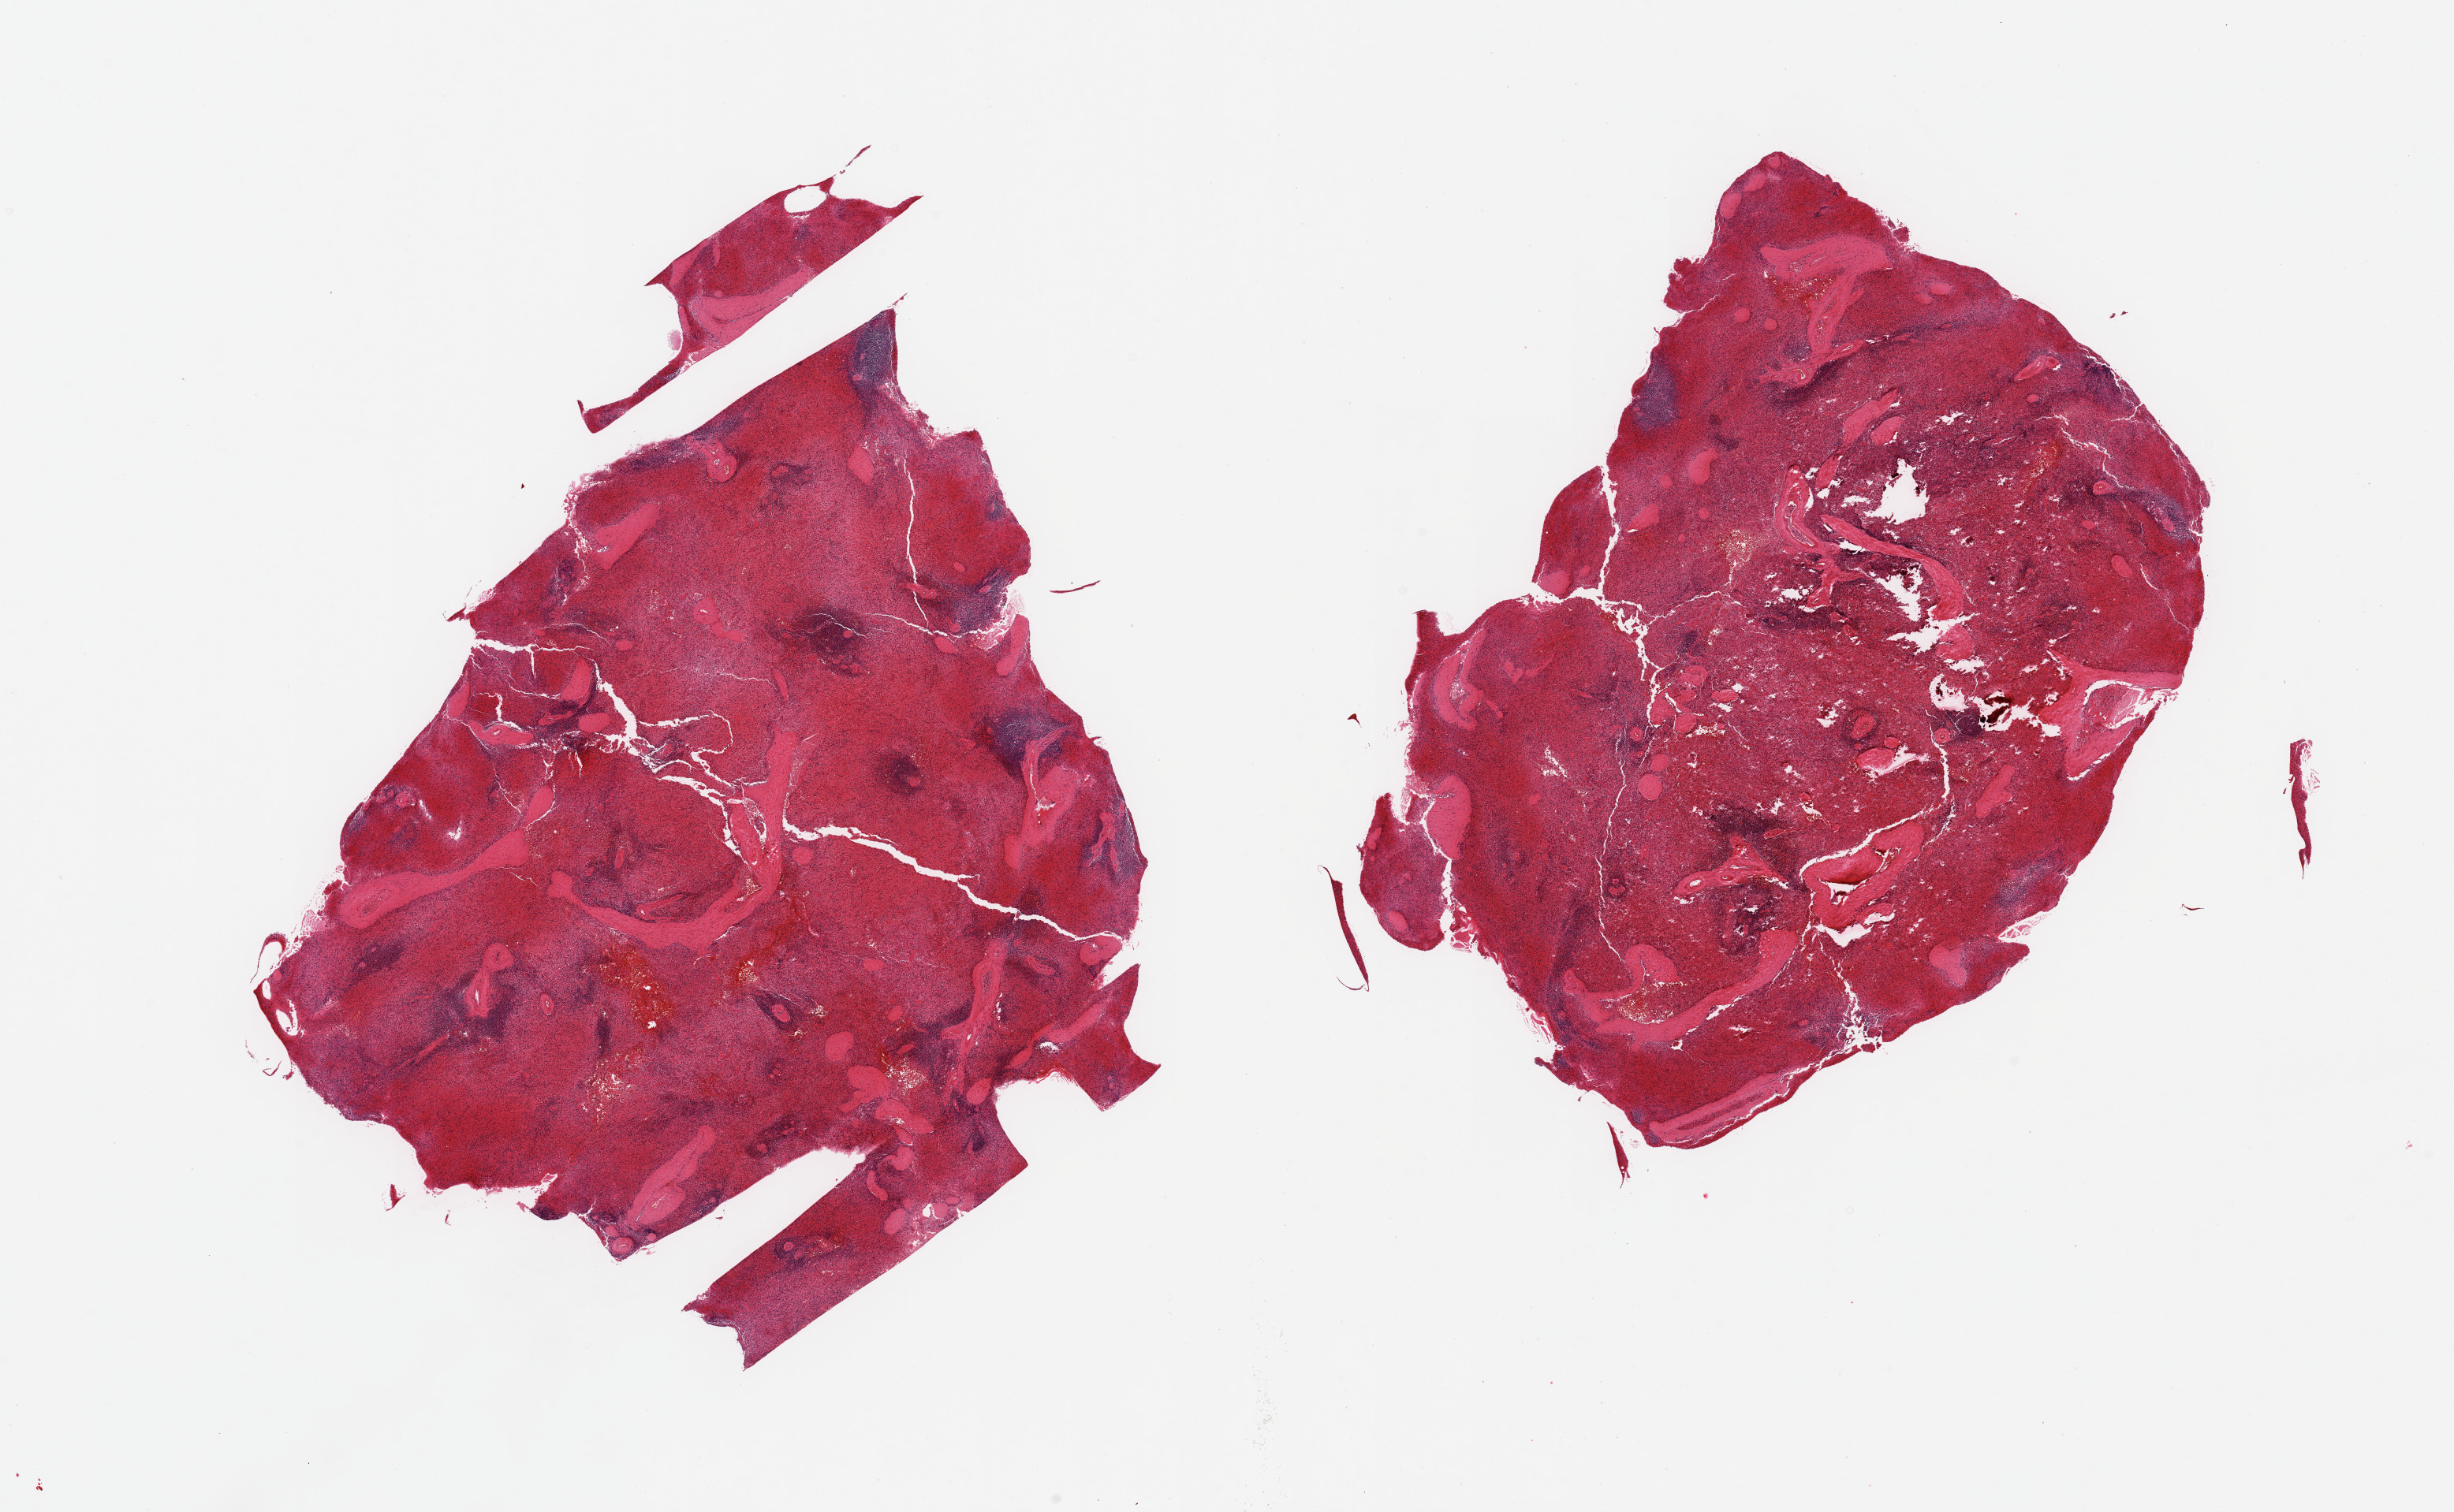
Haematoxylin and eosin whole-slide image — low-resolution overview of the scanned area, about 24.6 x 15.2 mm (slide scanned at 20x), PAXgene-fixed paraffin-embedded (PFPE) section, section of spleen (target tissue), tissue donor sample. Donor sex: male.
Review note (as recorded): 2 pieces; congested.